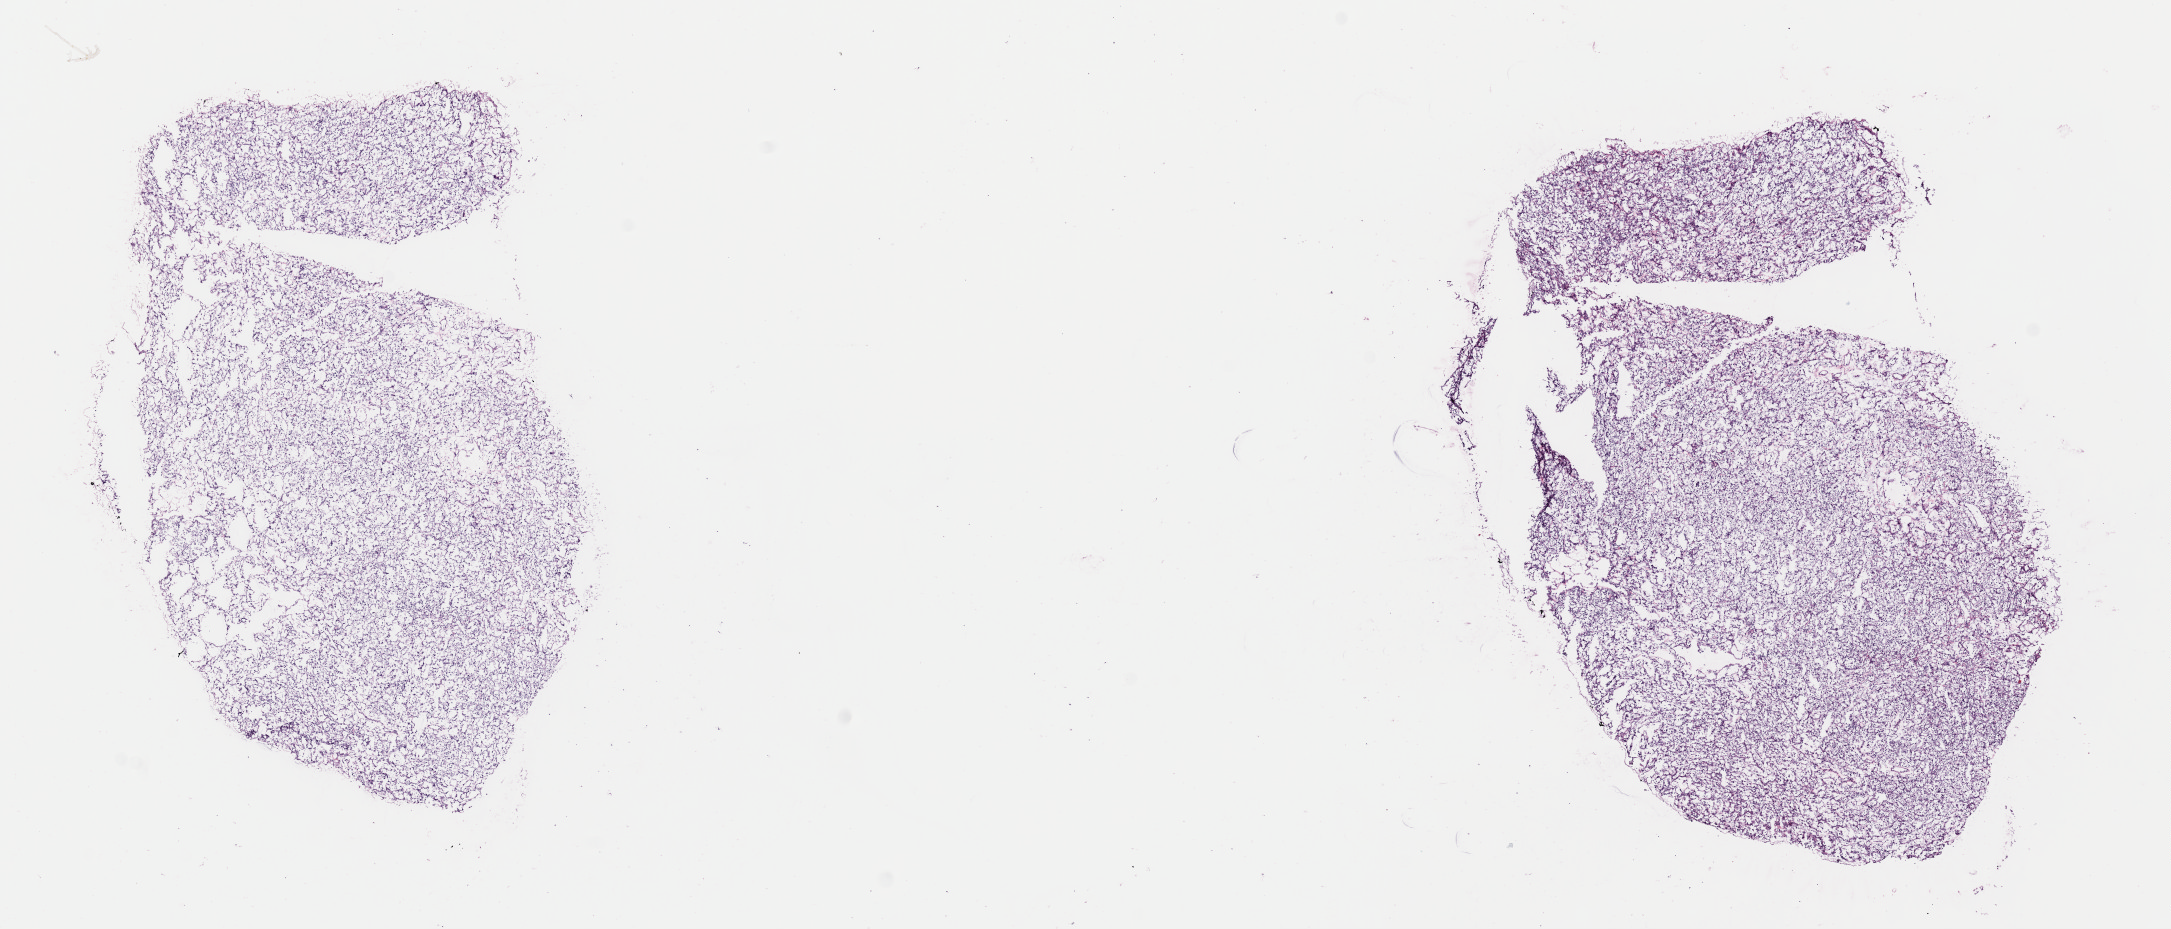
Whole-slide histology image, H&E-stained — whole scanned area (about 17.2 x 7.3 mm, acquisition: 40x scan) shown as a low-resolution overview, frozen section from the top of the tissue portion, kidney, primary tumour sample. Female, age 49 years at initial diagnosis. Histologic grade: G2 (moderately differentiated). Slide review estimates, as recorded: tumour cells 85%, tumour nuclei 85%, normal cells 0%, stromal cells 15%, necrosis 0%. Infiltration values recorded for this section: lymphocyte infiltration 0%, monocyte infiltration 0%, neutrophil infiltration 0%.
AJCC pathologic stage: I (7th edition). Histologic diagnosis: Renal cell carcinoma, NOS.